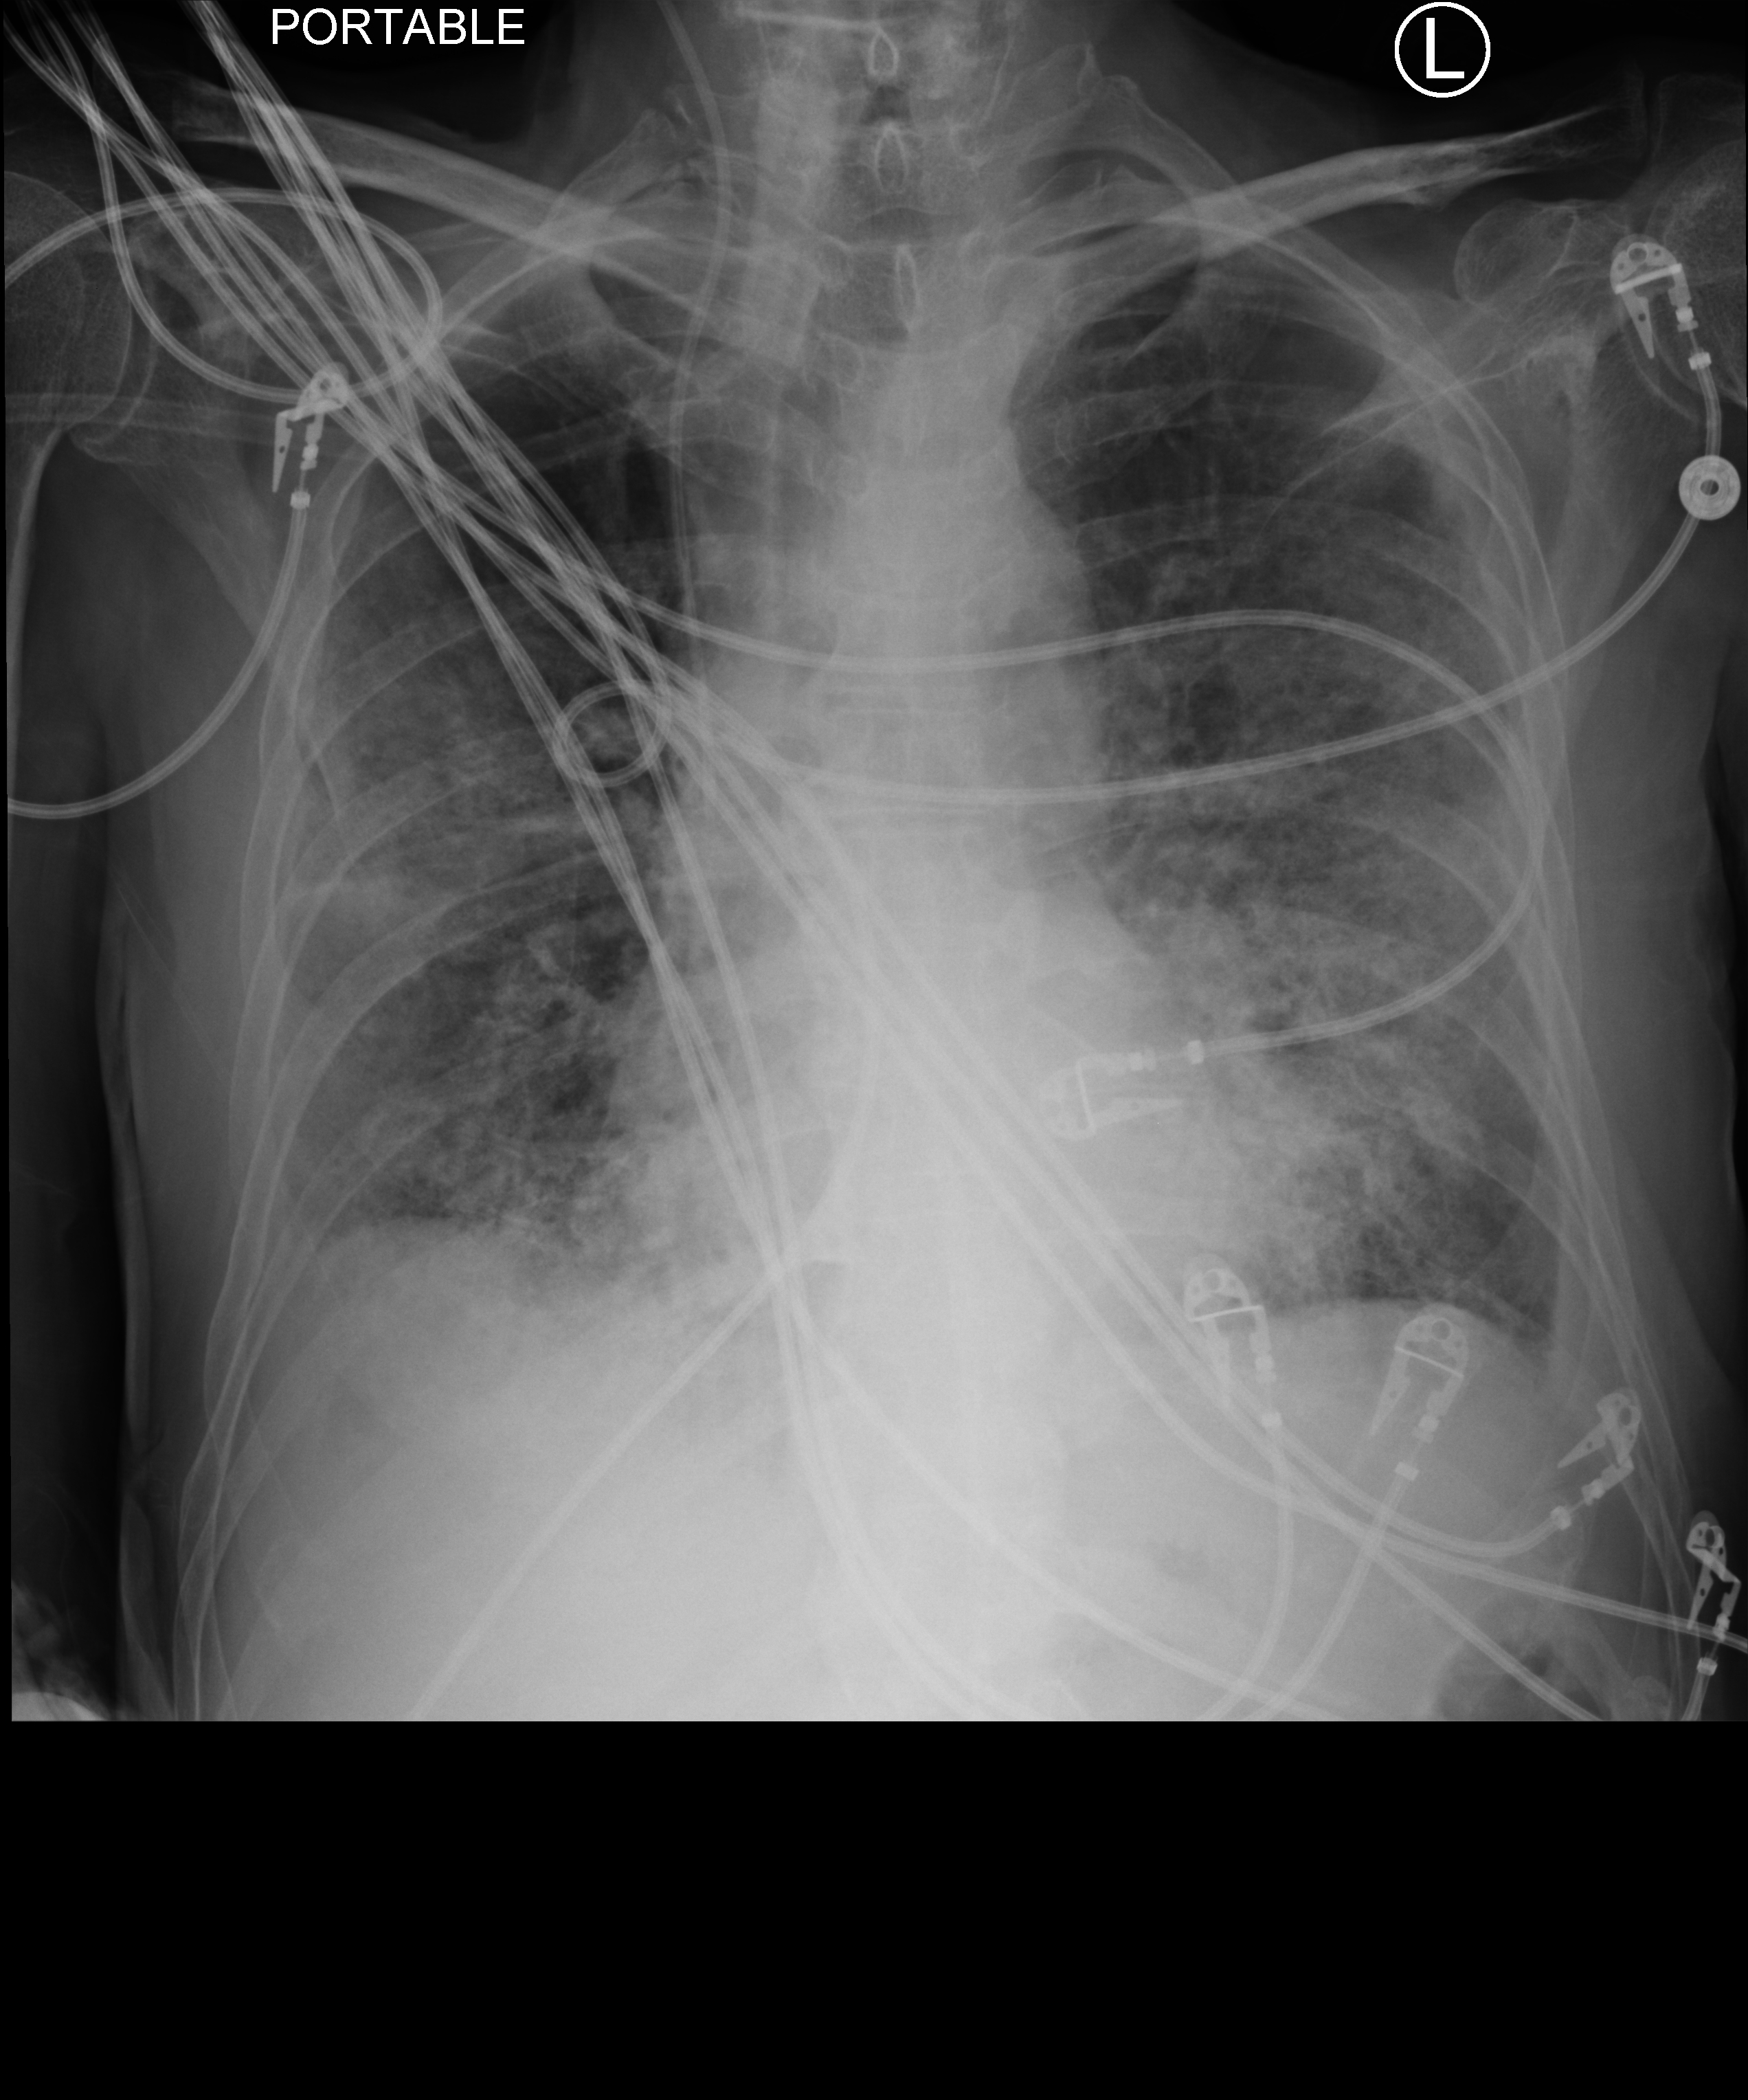
Portable chest radiograph; anteroposterior (AP) projection. Patient hospitalised with COVID-19; male, aged 60–74 years.
Hospital-stay facts (about this admission, not read from this image; timing relative to this image not recorded):
- length of hospital stay: 42 days
- admitted to intensive care during this hospital stay: yes